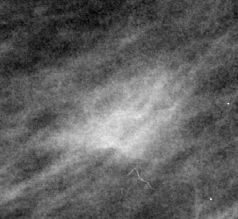
Cropped region of a digitized screen-film mammogram centred on a radiologist-marked abnormality, right breast, MLO view, BI-RADS breast density category 1 (scale 1–4).
Finding: mass, shape oval, margins ill defined; BI-RADS assessment category 4; pathology (as recorded): malignant.